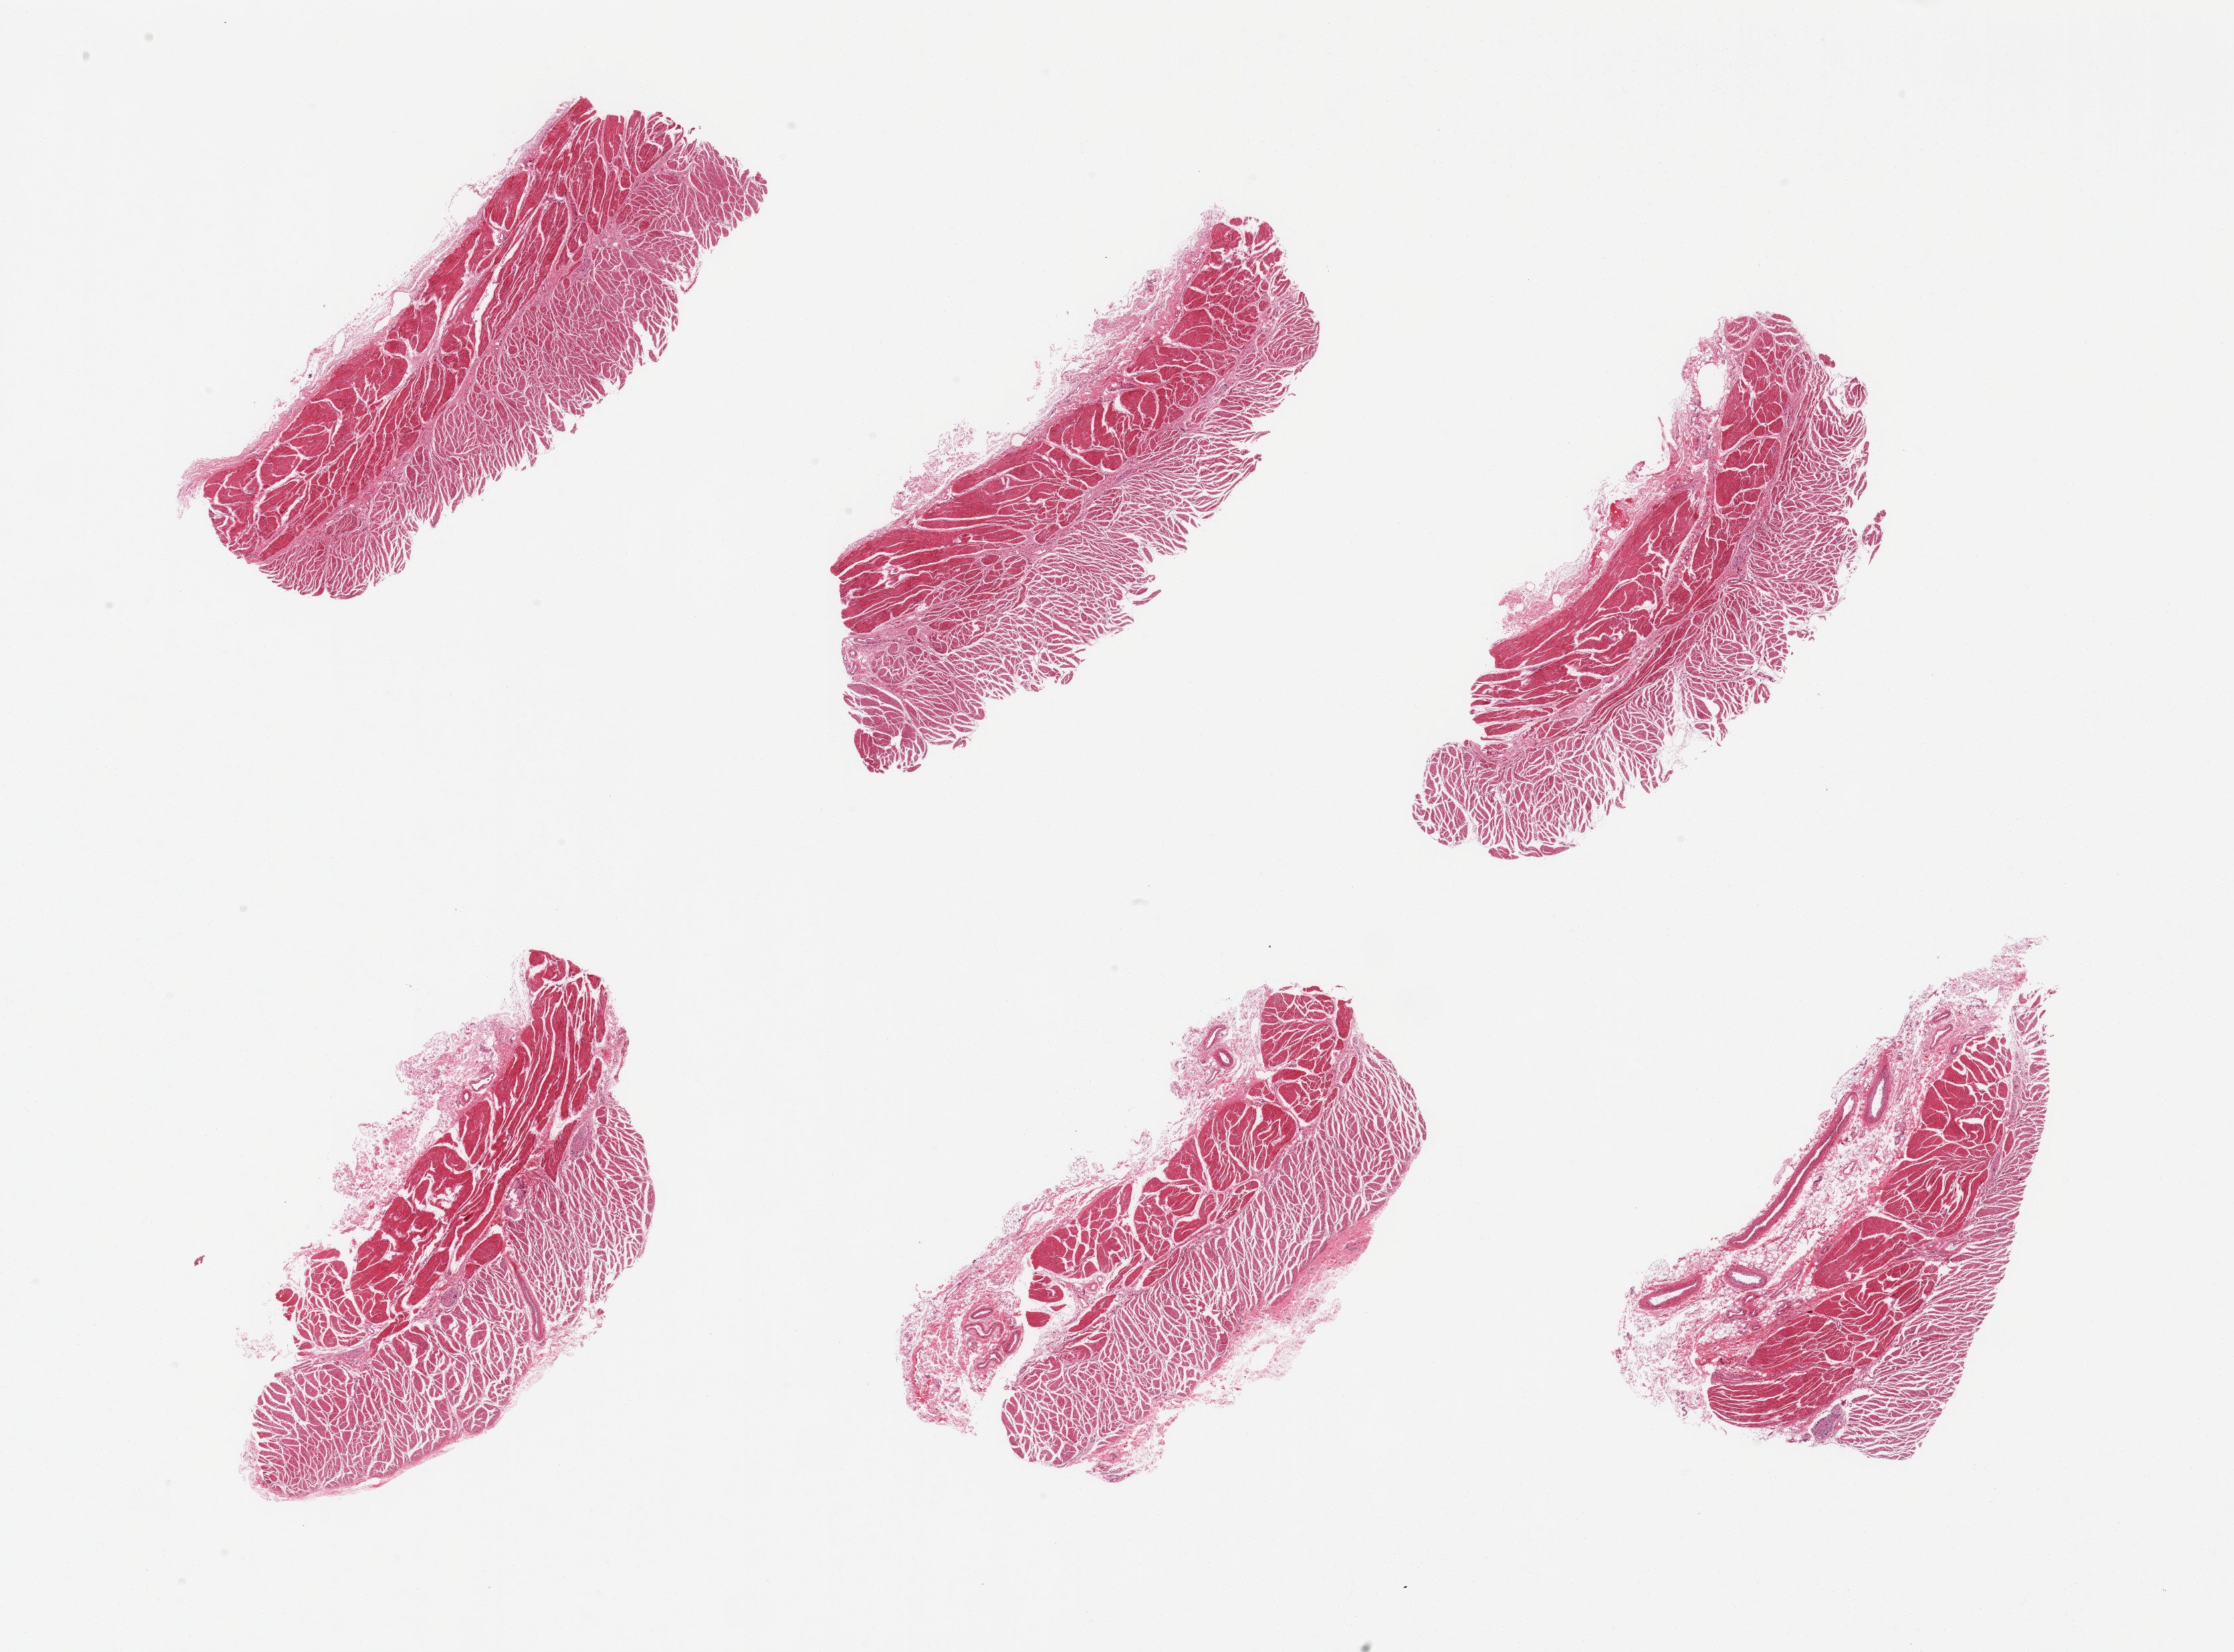
Digitized hematoxylin and eosin (H&E)-stained section, brightfield, a low-resolution overview of the entire scanned area, about 26.6 x 19.7 mm. PAXgene-fixed paraffin-embedded (PFPE) section. Sampled site (target tissue): gastroesophageal junction. Tissue donor sample.
Reviewer comment on this tissue sample: 6 pieces; target muscularis, some residual attached fat/large vessels.